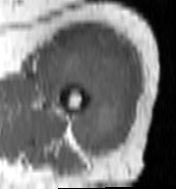
MRI of an extremity soft-tissue mass, one axial slice; position 76 of 100 along the scan axis; MR volume resampled by the dataset authors to the PET/CT grid (not the native acquisition matrix); 3.27 mm slice thickness; 176 × 189 image matrix, field of view 172 × 185 mm. Female patient. Case-level facts recorded for this patient, not image findings: histological type: undifferentiated – high grade; grade: high; site of the primary tumour: left thigh.
Annotated regions visible in this slice (expert contour drawn on MRI and transferred to this co-registered scan by the dataset authors):
- gross tumour volume including surrounding oedema: bounding box [x1, y1, x2, y2] px = [46, 39, 131, 158]
- gross tumour volume (mass): [48, 41, 131, 158]